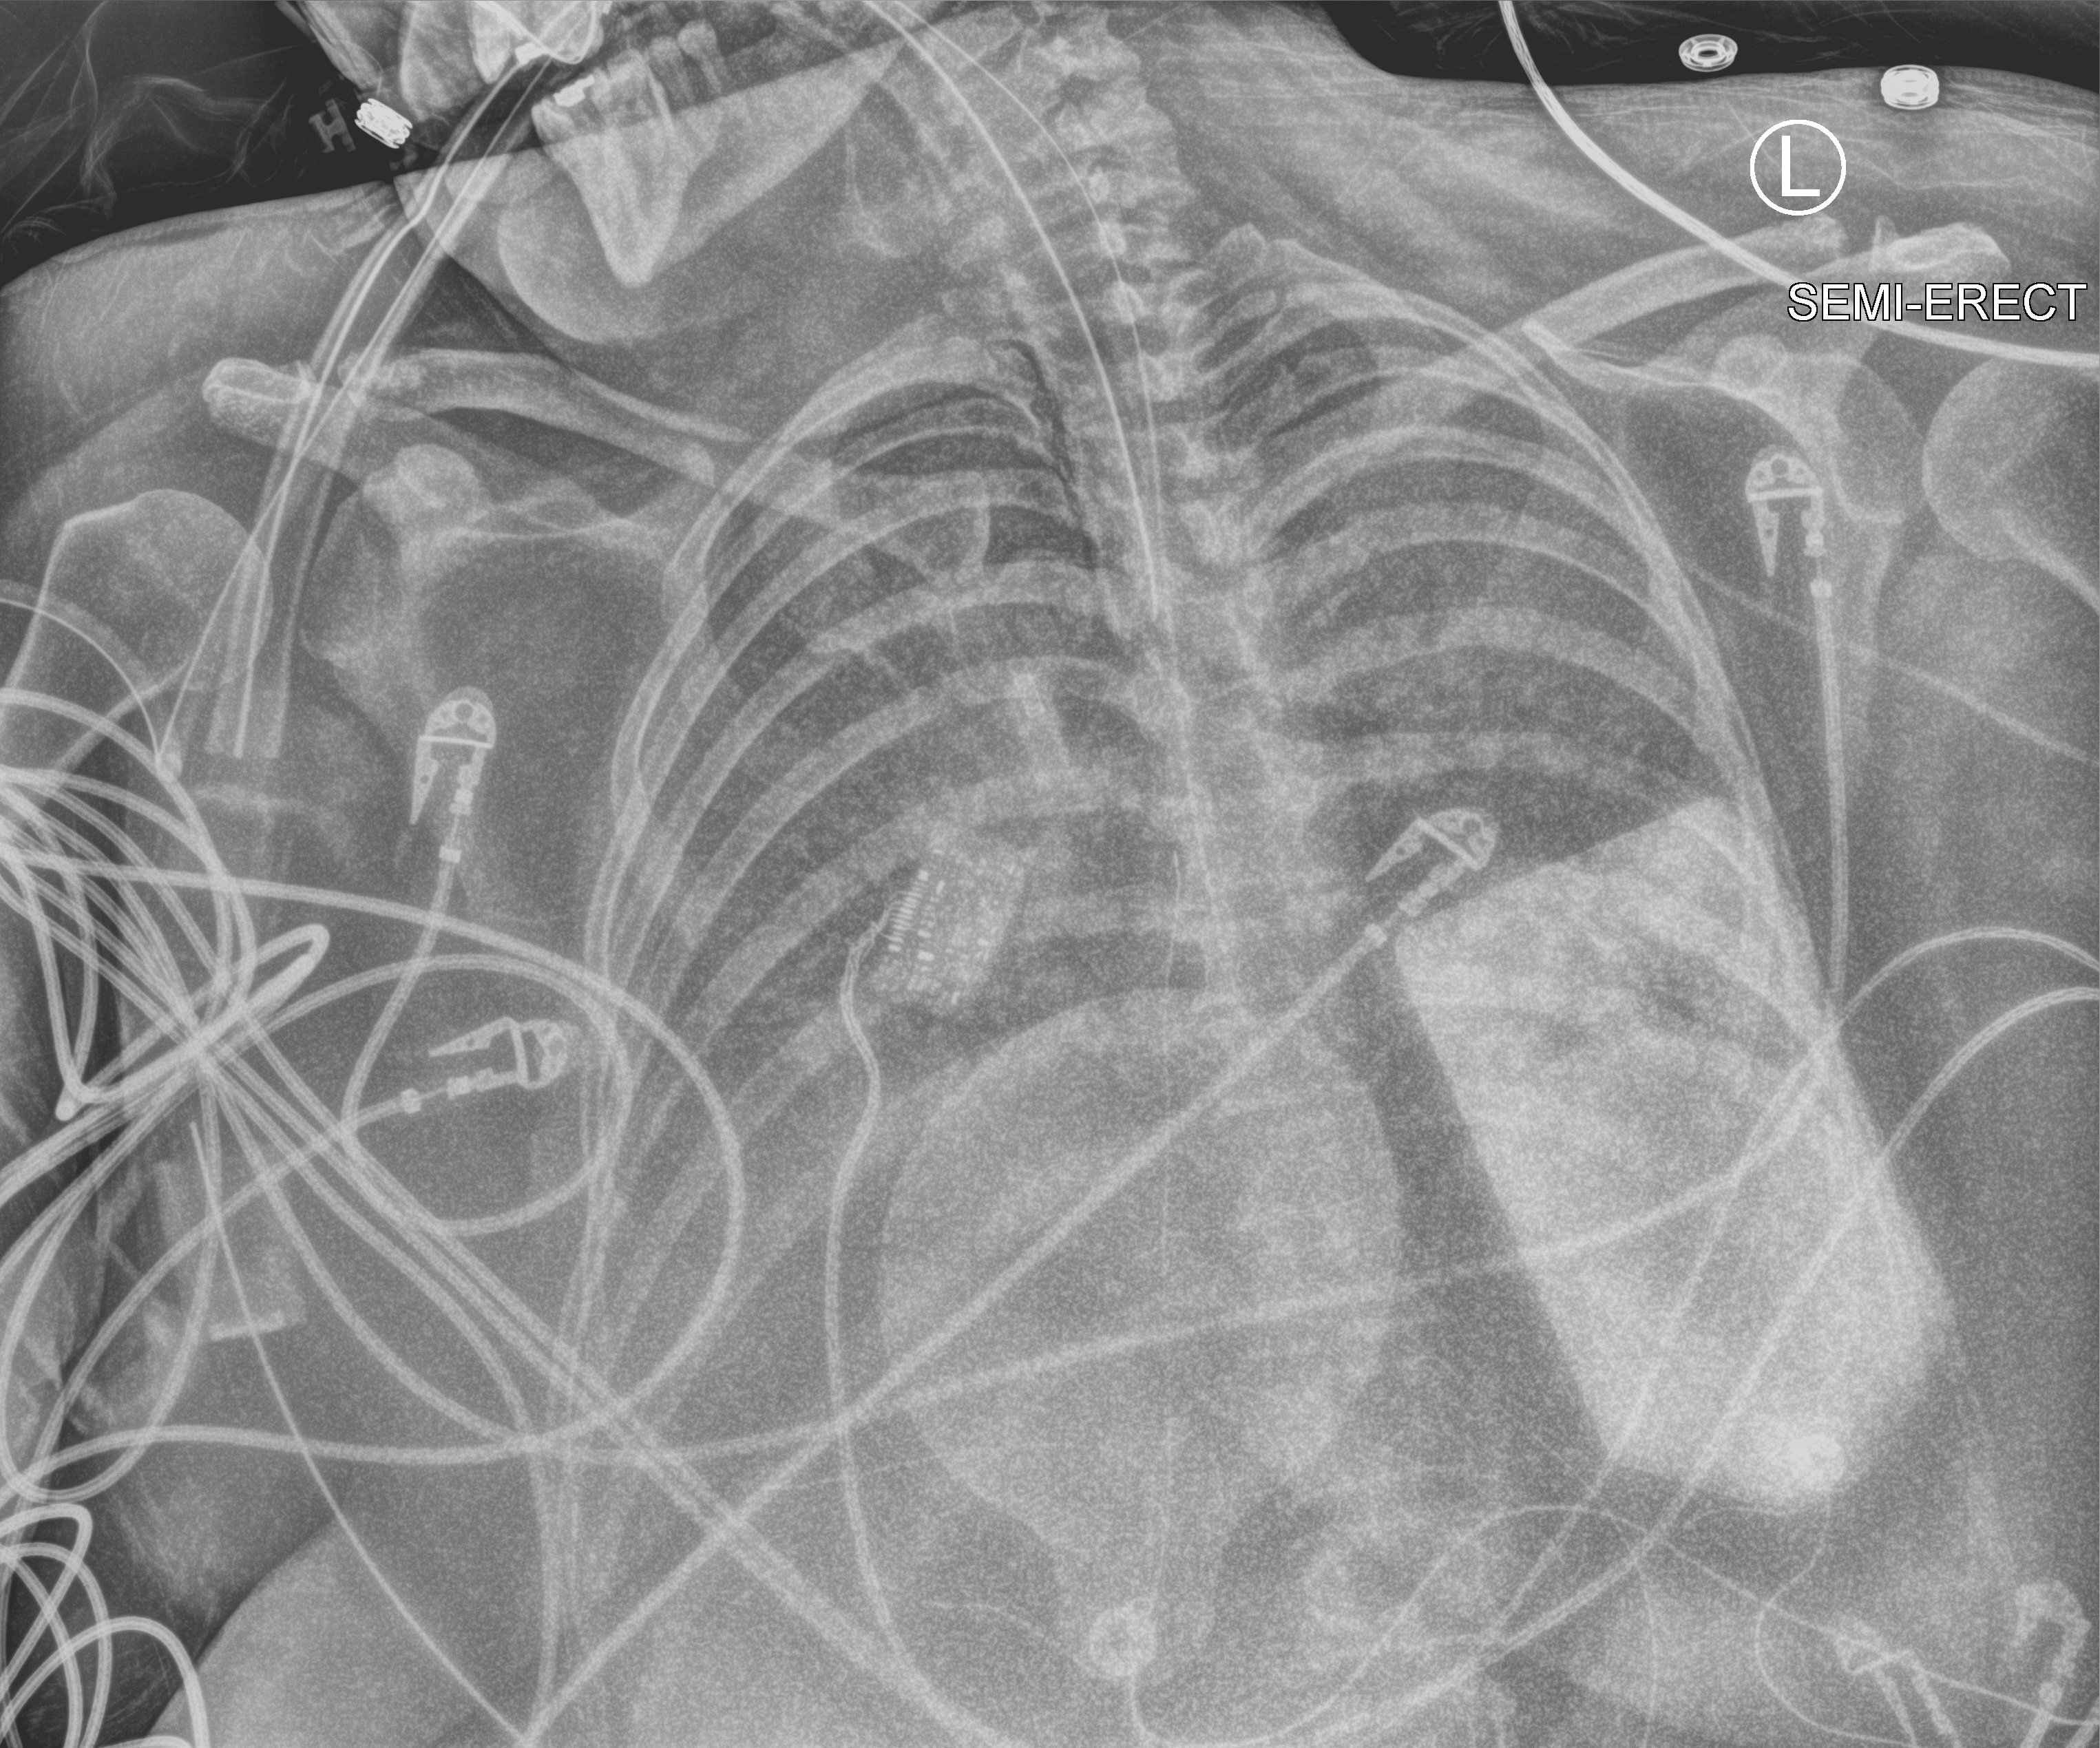
Chest X-ray (portable), anteroposterior (AP) projection. Female patient hospitalised with COVID-19, age 18–59 years.
Hospital-stay facts (about this admission, not read from this image; timing relative to this image not recorded):
- mechanically ventilated during this hospital stay: yes
- admitted to intensive care during this hospital stay: yes
- length of hospital stay: 95 days